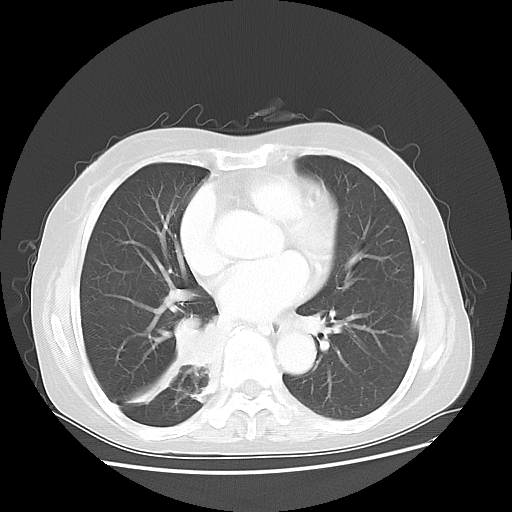
Chest CT, one axial slice; reconstruction kernel LUNG; lung window (W 1500 / L -600 HU); 512 × 512 image matrix, field of view 360 × 360 mm. Female patient, age 63 years. From the clinical record (not read from this slice): clinical TNM (as recorded): T2 N3 M1b.
Outlined on this slice (rectangle marked by the reading radiologist):
- lung tumour (recorded histology: small cell carcinoma): bounding box [x1, y1, x2, y2] px = [167, 309, 230, 393]